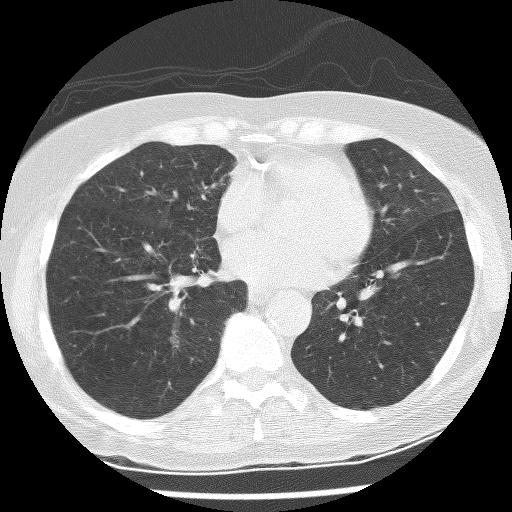
Low-dose screening chest CT, one axial slice. Slice 105 of 247 in the series (ordered by position). Reconstruction kernel BONE. Lung window (W 1500 / L -600 HU). 512 × 512 image matrix, field of view 300 × 300 mm.
Structures marked on this image (outlined manually by an expert reader):
- lesion 1 (tumor, lower lobe of right lung): box from (x=171, y=330) to (x=179, y=347) px